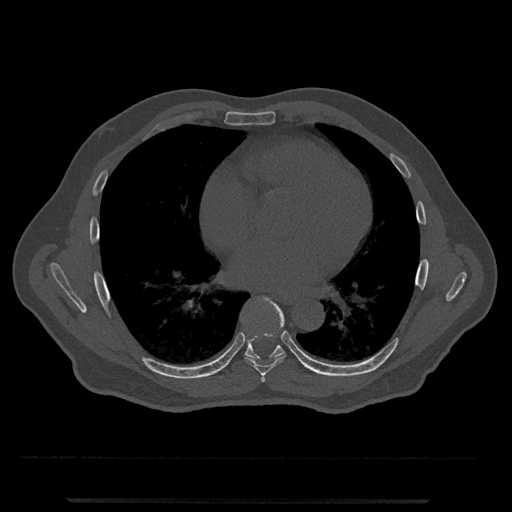
CT including the spine, one axial slice; position 659 of 797 along the scan axis; 120 kVp; bone window (W 1800 / L 400 HU); 512 × 512 image matrix, field of view 419 × 419 mm. Patient: male, 63 years. From the clinical record (not read from this slice): primary cancer: prostate.
Structures marked on this image (semi-automatically segmented with operator editing):
- T6 vertebra: bounding box [x1, y1, x2, y2] px = [261, 376, 265, 382]
- T7 vertebra: [244, 298, 286, 376]
- T8 vertebra: [245, 312, 285, 360]